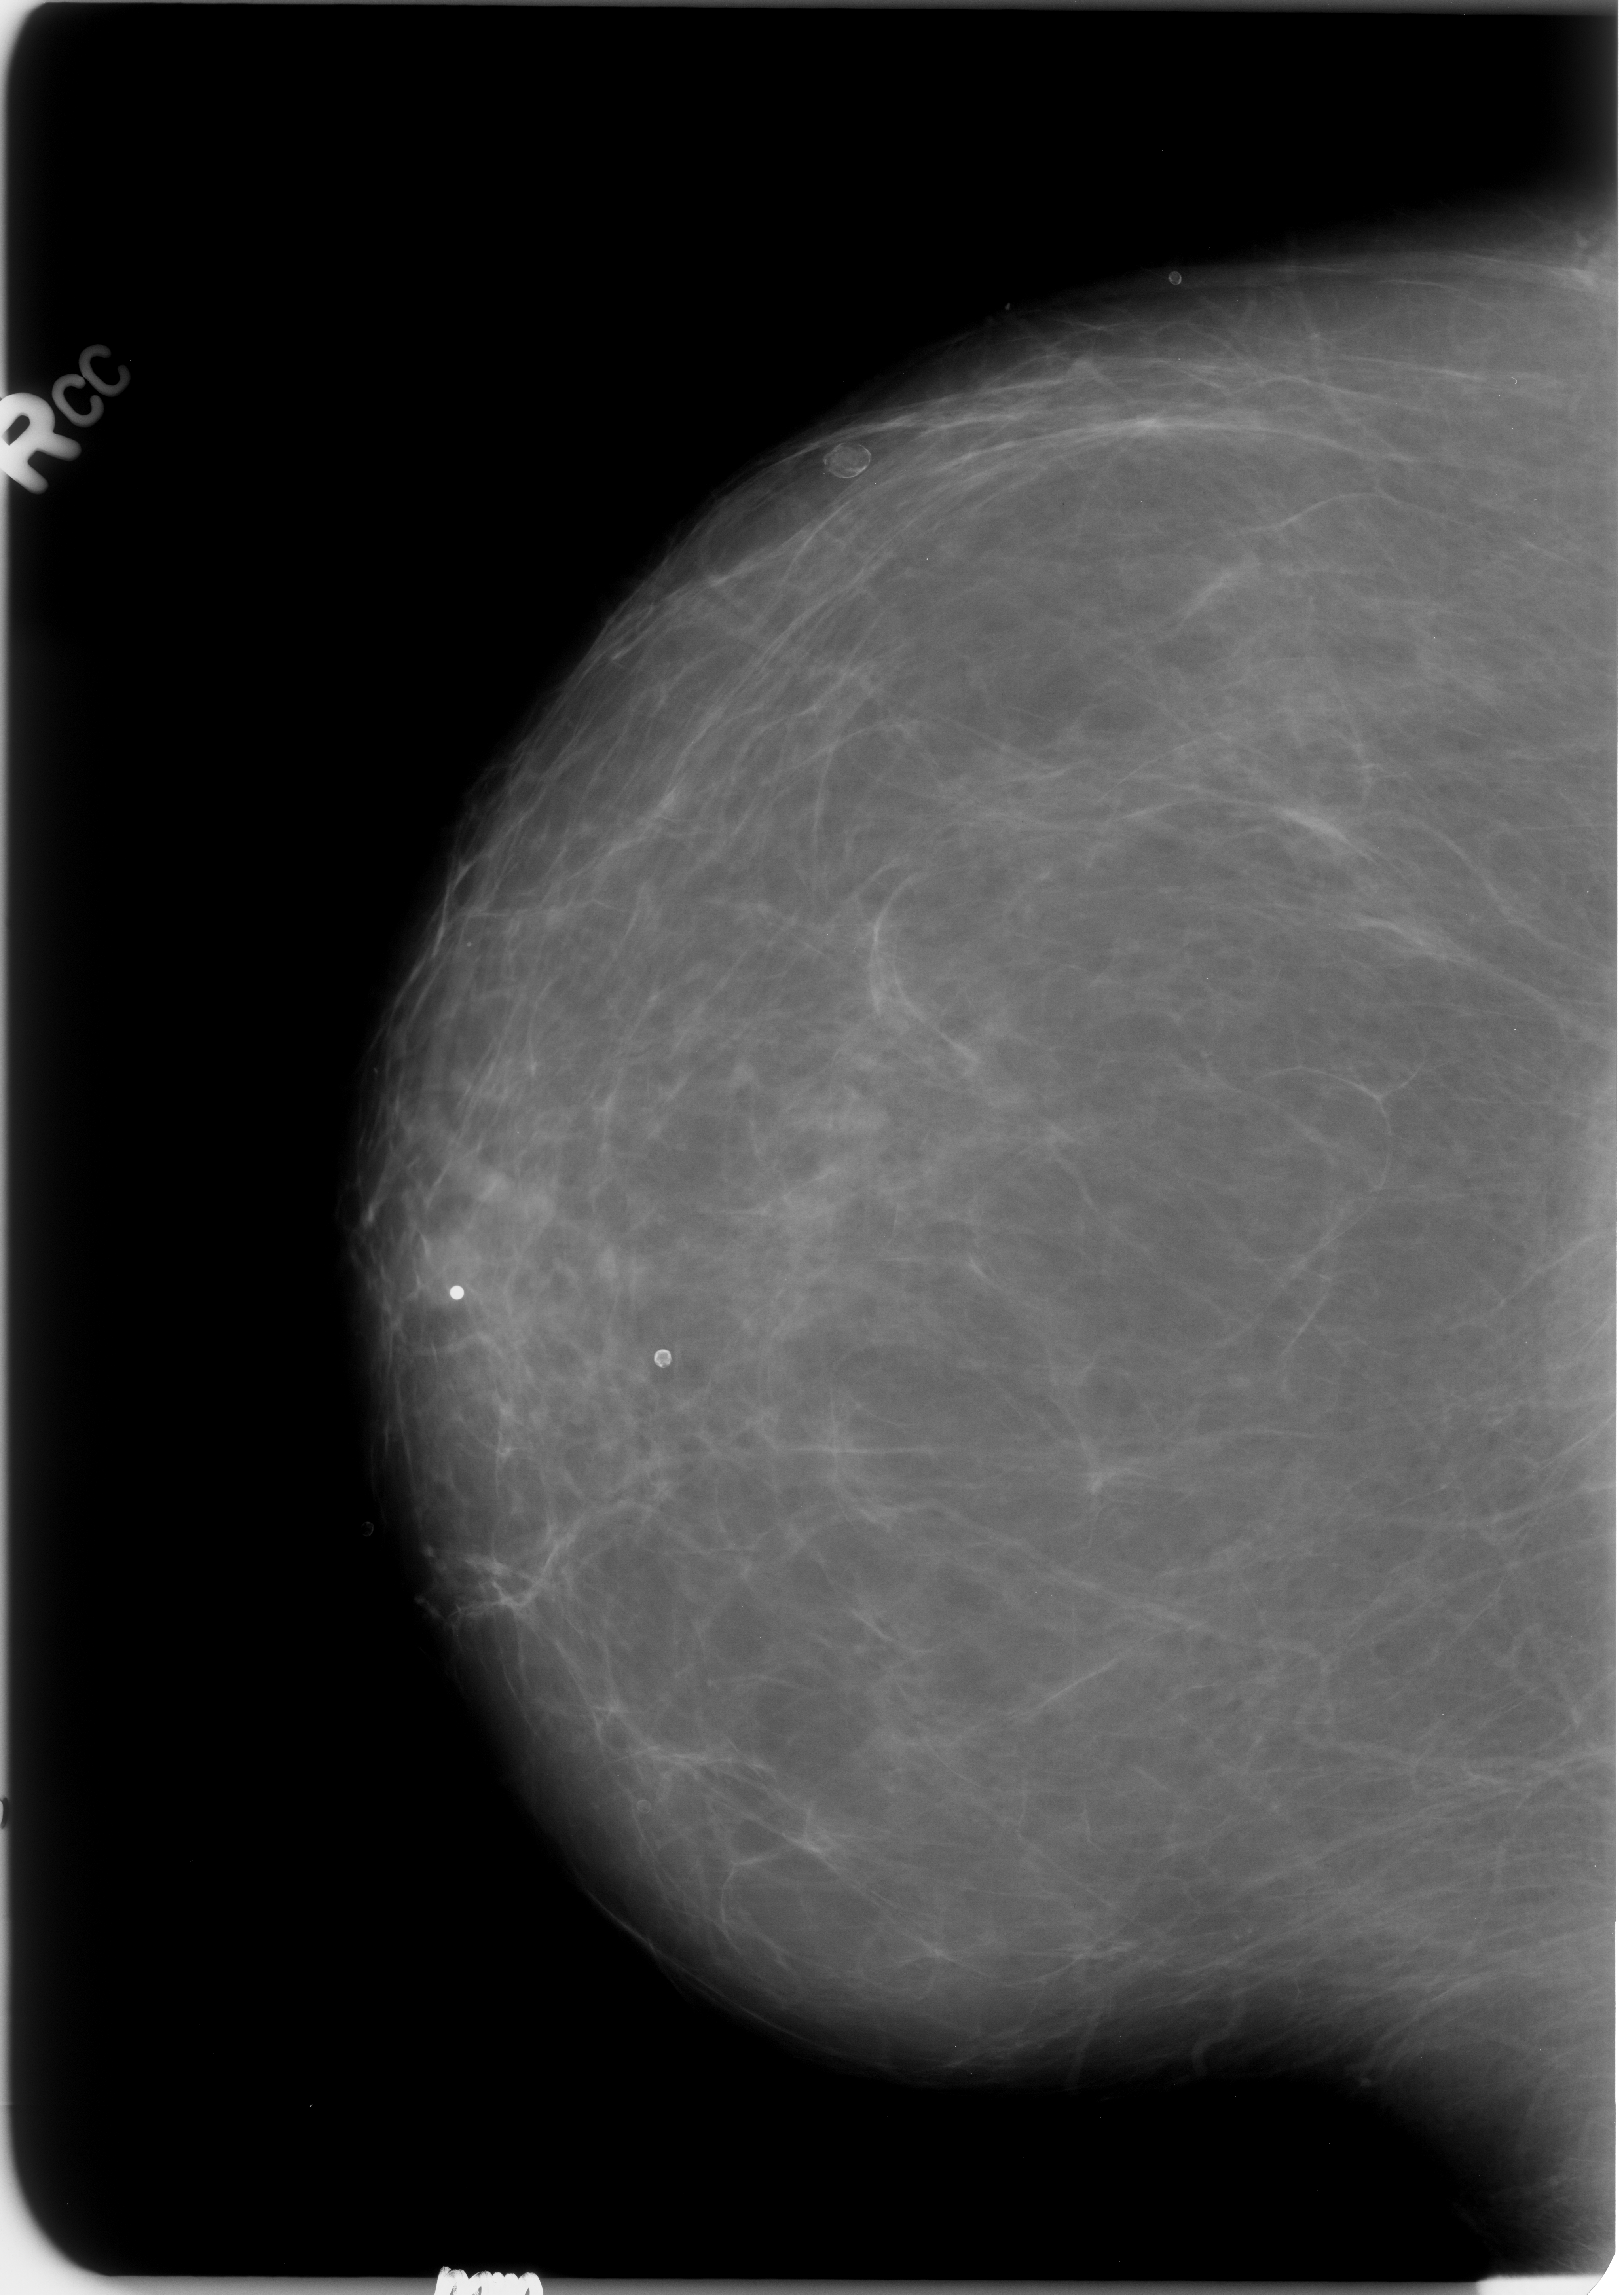
Scanned film-screen mammogram, right breast, CC view.
Abnormality record for this image: Finding 1 of 3: calcifications, morphology eggshell; BI-RADS assessment category 2; subtlety rating 5 on a 1 (subtle) to 5 (obvious) scale; benign without callback (not worked up further). Finding 2 of 3: calcifications, morphology lucent center; BI-RADS assessment category 2; subtlety rating 5 on a 1 (subtle) to 5 (obvious) scale; benign; no additional work-up was recommended (benign without callback). Finding 3 of 3: calcifications, morphology lucent center; BI-RADS assessment category 2; benign without callback (not worked up further).